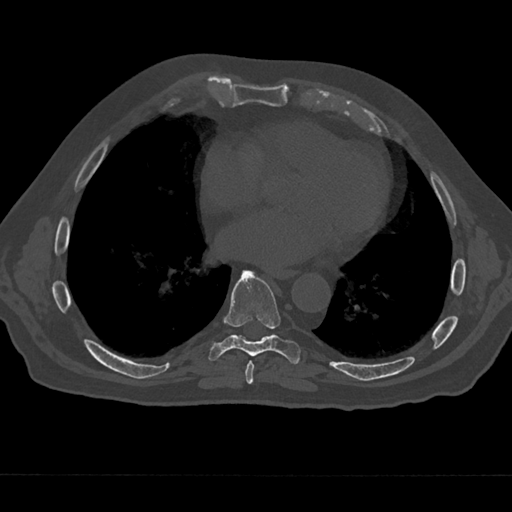
CT including the spine, one axial slice. Position 318 of 797 along the scan axis. Bone window (W 1800 / L 400 HU). 0.5 mm slice thickness. 512 × 512 image matrix, field of view 377 × 377 mm. Patient: male, 75 years. From the clinical record (not read from this slice): primary cancer: renal; vertebrae with lytic lesions (as recorded): T4.
Outlined on this slice (semi-automatically segmented with operator editing):
- T7 vertebra: bounding box [x1, y1, x2, y2] px = [243, 360, 255, 385]
- T8 vertebra: [208, 270, 300, 365]